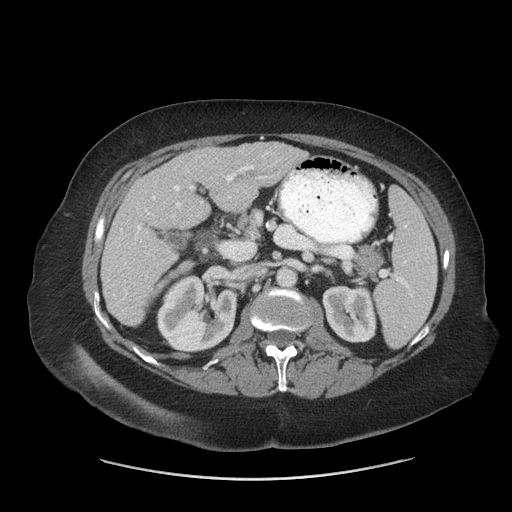
Contrast-enhanced abdominal CT (liver protocol), one axial slice. Position 29 of 69 along the scan axis. Reconstruction kernel STANDARD. Soft-tissue window (W 400 / L 40 HU). 2.5 mm slice thickness. 512 × 512 image matrix, field of view 420 × 420 mm. From the clinical record (not read from this slice): diagnosis: hepatocellular carcinoma (patient treated with transarterial chemoembolisation; whether this scan precedes or follows treatment is not stated here); TNM stage (as recorded): Stage-IIIB; Child-Pugh class: A; tumour nodularity: multinodular.
Structures marked on this image (semi-automatic segmentation, software-assisted and operator-edited):
- liver parenchyma outside the tumour (the mass and vessels are separate outlines, so this box may not span the whole liver): bounding box (x1, y1, x2, y2) in pixels: (100, 142, 307, 326)
- liver vessels: (120, 153, 267, 299)